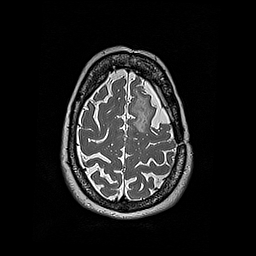
Brain MRI from a brain-tumour surgery series, one axial slice. Slice 145 of 192 in the series (ordered by position). 256 × 256 image matrix. Case-level facts recorded for this patient, not image findings: histopathology: Oligodendroglioma; WHO grade: 2; IDH mutation: yes; tumour location: Left Frontal.
Outlined on this slice (expert manual segmentation):
- tumour: bounding box <146,112,153,125> (left, top, right, bottom; pixels)